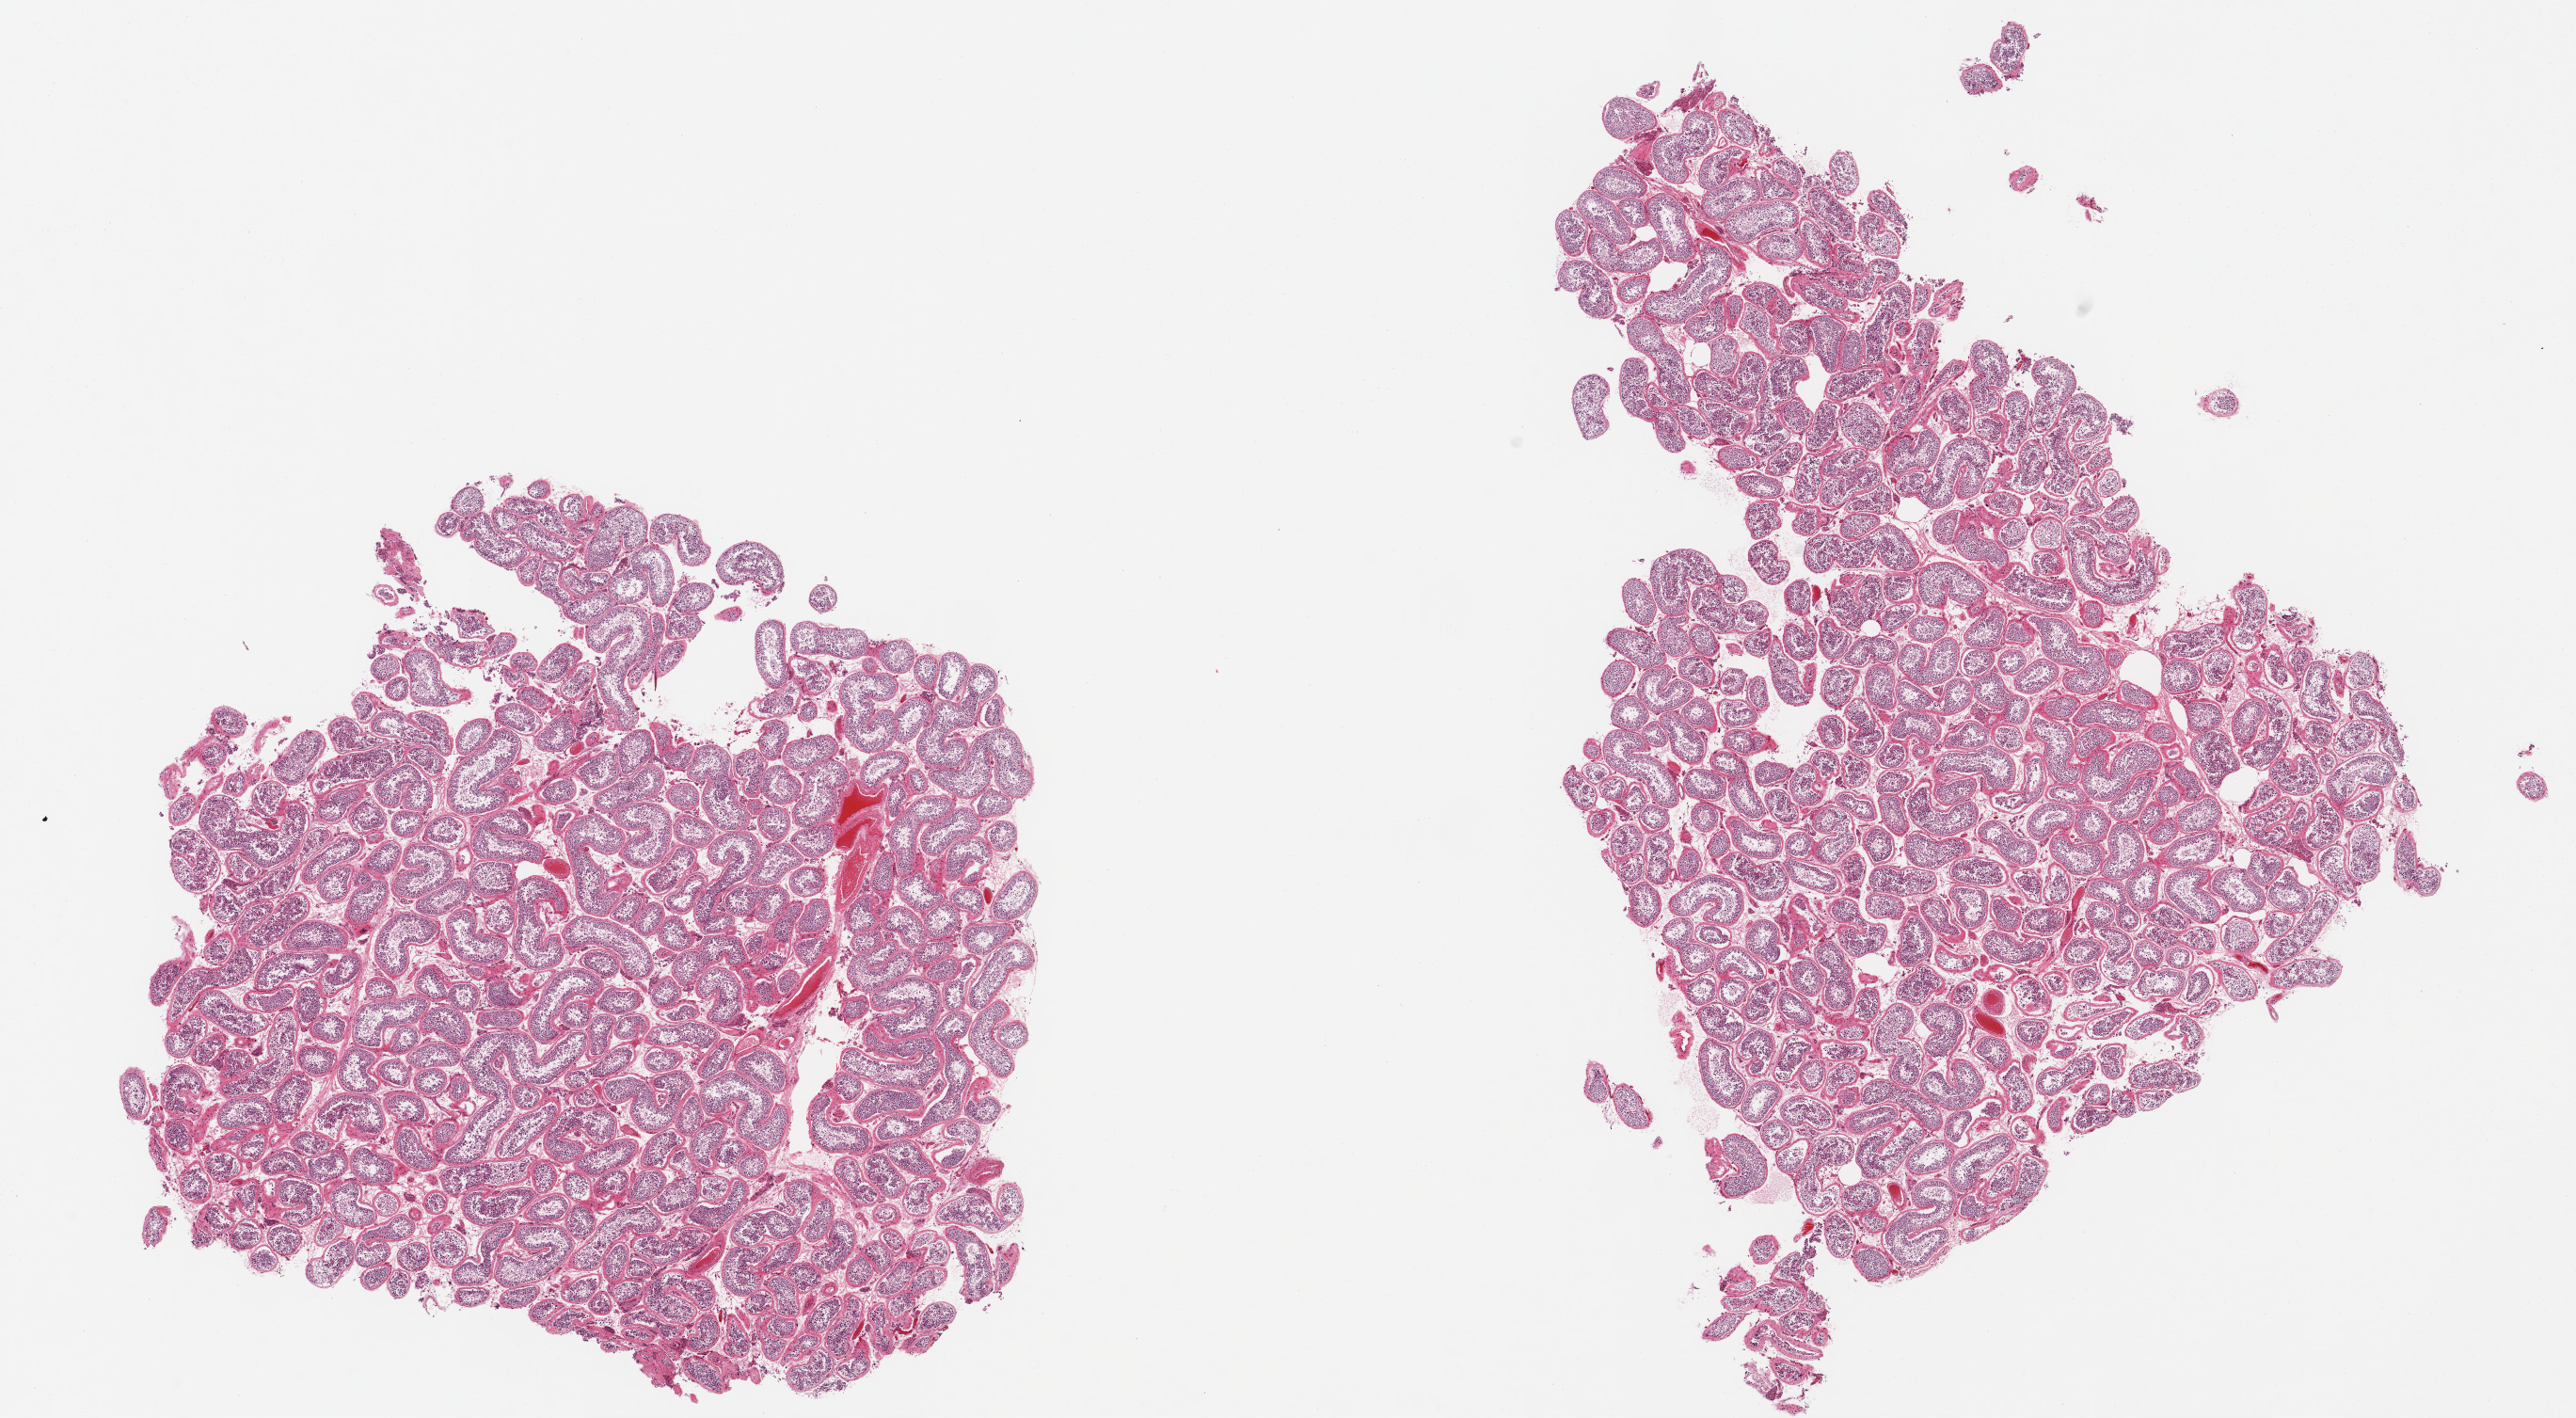
Hematoxylin and eosin (H&E) whole-slide image, low-resolution overview of the scanned area, about 21.7 x 11.9 mm (slide scanned at 20x), PAXgene-fixed, paraffin-embedded tissue, target tissue: testis, tissue donor sample.
Pathologist's review note for this sample: 2 pieces, spermatogenesis appears reduced.